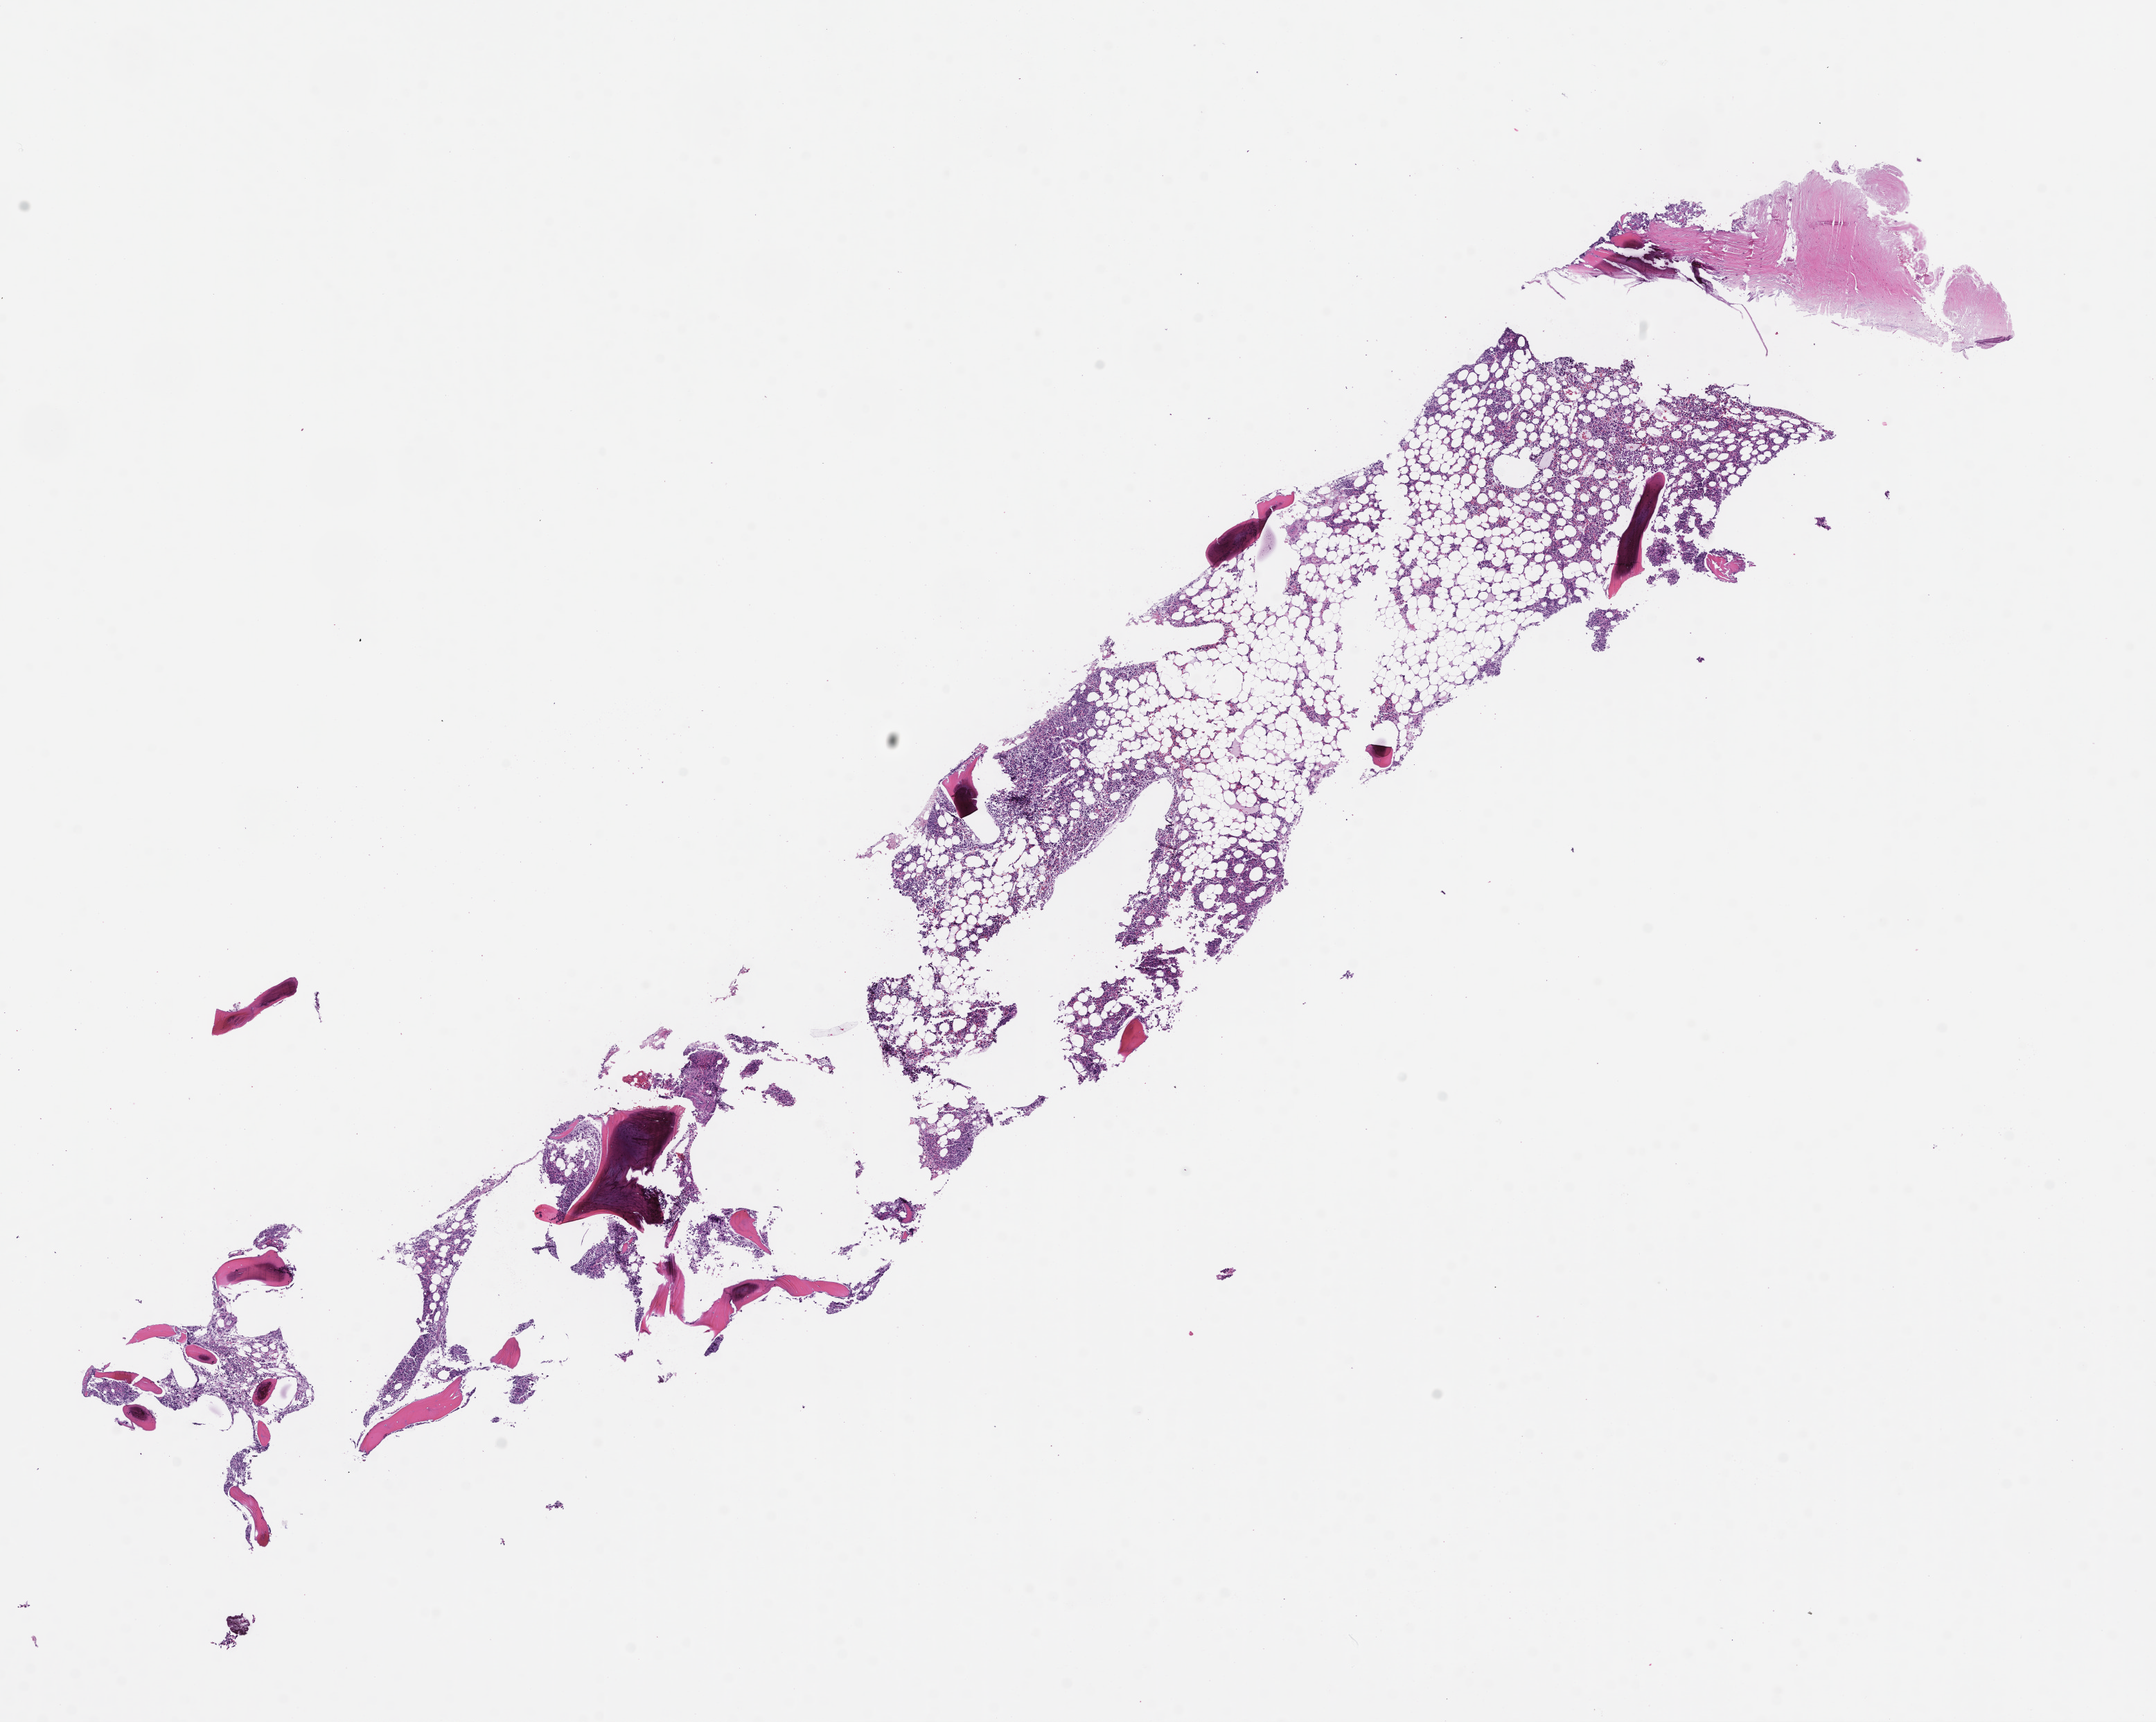
Digitized hematoxylin and eosin (H&E)-stained section, low-resolution overview of the scanned area, about 12.6 x 10.0 mm, FFPE section, tissue site: bone marrow, archival tissue. Patient sex: female.
This section: primary tumor. Diagnosis: Plasma Cell Myeloma.